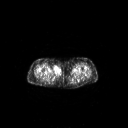
FDG PET of an extremity soft-tissue mass (from a PET/CT study), one axial slice; position 236 of 311 along the scan axis; 3.27 mm slice thickness; 128 × 128 image matrix, field of view 700 × 700 mm. Female patient, age 78 years. Case-level facts recorded for this patient, not image findings: histological type: leiomyosarcoma; grade: intermediate; site of the primary tumour: parascapusular.
Outlined on this slice (expert contour drawn on MRI and transferred to this co-registered scan by the dataset authors):
- gross tumour volume including surrounding oedema: bounding box <53,66,62,75> (left, top, right, bottom; pixels)
- gross tumour volume (mass): <53,66,62,75>